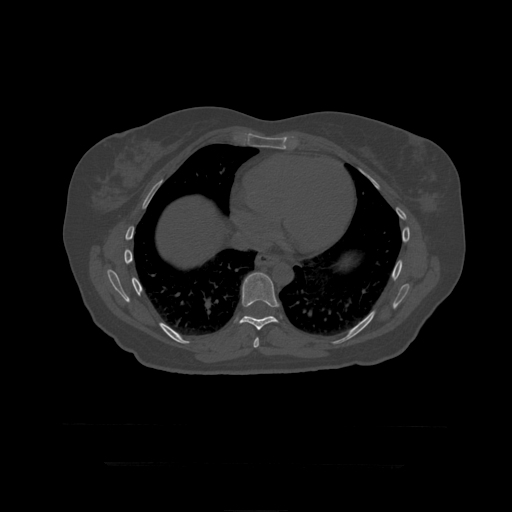
CT including the spine, one axial slice. Reconstruction kernel STANDARD. Bone window (W 1800 / L 400 HU). 1.25 mm slice thickness. 512 × 512 image matrix, field of view 450 × 450 mm. Patient age 41 years. From the clinical record (not read from this slice): primary cancer: breast.
Structures marked on this image (semi-automatically segmented with operator editing):
- T10 vertebra: box from (x=248, y=316) to (x=272, y=318) px
- T8 vertebra: (x=254, y=337)–(x=259, y=348)
- T9 vertebra: (x=239, y=273)–(x=280, y=330)